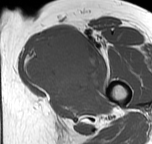
MRI of an extremity soft-tissue mass, one axial slice; slice 40 of 57 in the series (ordered by position); MR volume resampled by the dataset authors to the PET/CT grid (not the native acquisition matrix); 3.27 mm slice thickness; 152 × 144 image matrix, field of view 148 × 141 mm. Female patient. Case-level facts recorded for this patient, not image findings: histological type: pleiomorphic leiomyosarcoma; grade: intermediate; site of the primary tumour: left thigh.
Structures marked on this image (expert contour drawn on MRI and transferred to this co-registered scan by the dataset authors):
- gross tumour volume including surrounding oedema: bounding box (x1, y1, x2, y2) in pixels: (25, 30, 101, 95)
- gross tumour volume (mass): (25, 30, 101, 95)